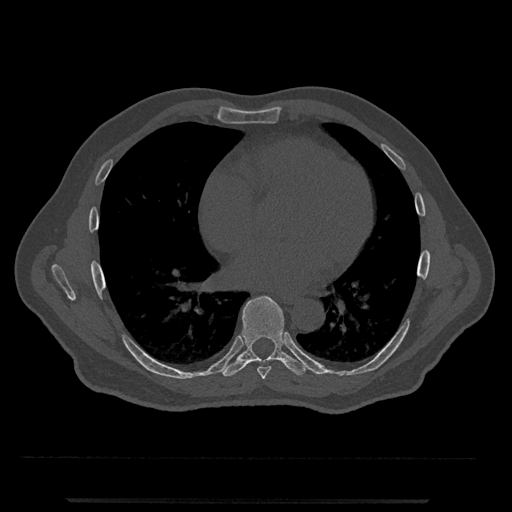
CT including the spine, one axial slice; position 648 of 797 along the scan axis; reconstruction kernel Br40s/3; 120 kVp; bone window (W 1800 / L 400 HU); 0.5 mm slice thickness; 512 × 512 image matrix, field of view 419 × 419 mm. Patient: male, 63 years. Case-level facts recorded for this patient, not image findings: primary cancer: prostate.
Outlined on this slice (semi-automatically segmented with operator editing):
- T7 vertebra: box from (x=257, y=367) to (x=271, y=380) px
- T8 vertebra: (x=222, y=296)–(x=308, y=377)